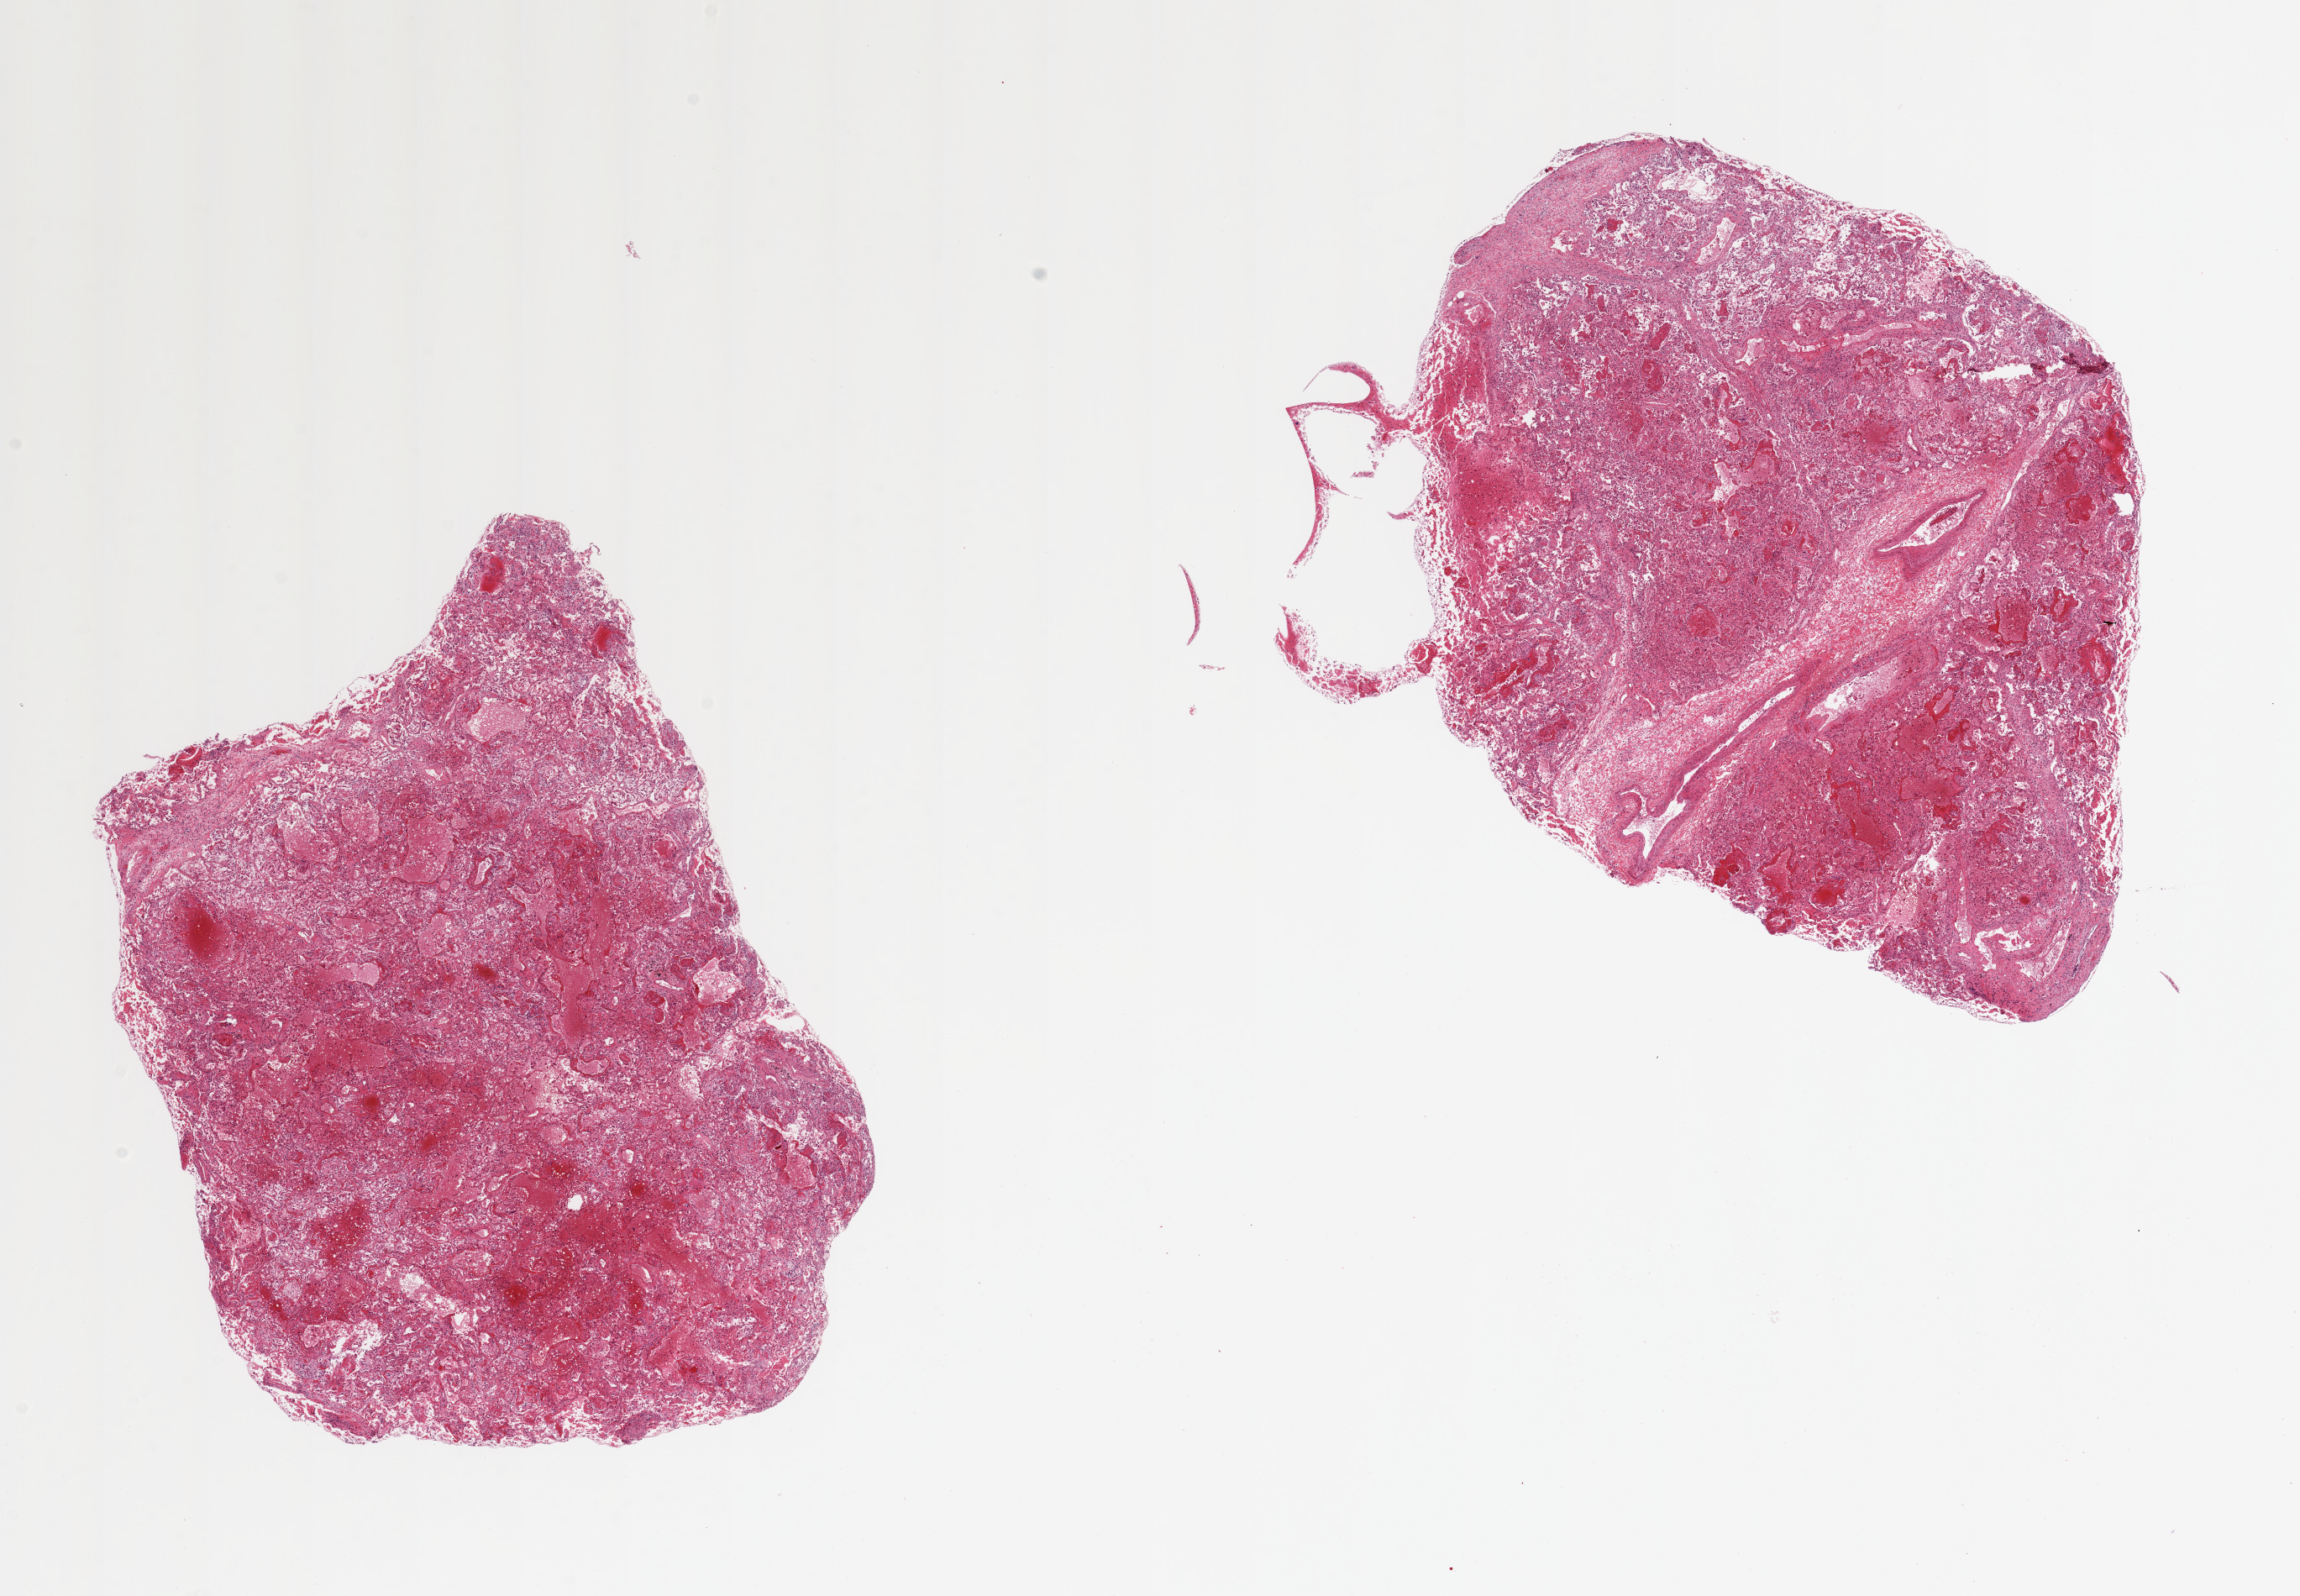
Whole-slide image, H&E stain, shown as a low-resolution overview of the whole scanned area (about 21.7 x 15.0 mm, acquisition: 20x scan); PAXgene-fixed, paraffin-embedded tissue; section of lung (target tissue); tissue donor sample.
* reviewer comment on this tissue sample: 2 pieces ~8x6mm, badly autolyzed, apparenty marked congestion